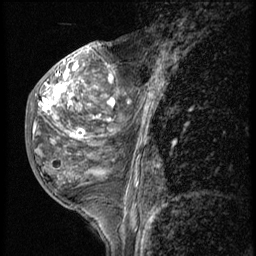
Breast MRI (dynamic contrast-enhanced), one sagittal slice; slice 22 of 56 in the series (ordered by position); 3 images stored at this slice position (order not interpretable as contrast timing); 1.5 T; TE 4.2 ms, TR 9 ms; 2.5 mm slice thickness; 256 × 256 image matrix, field of view 180 × 180 mm. Patient: female, 50 years. From the clinical record (not read from this slice): setting: breast cancer imaged before/during neoadjuvant chemotherapy; receptor status: triple-negative.
Outlined on this slice (semi-automatically segmented with operator editing):
- analysis volume of interest (the breast-tissue region the enhancement analysis was run in; not a lesion): box from (x=25, y=50) to (x=117, y=191) px
- tumour enhancement mask (voxels above the 140 % enhancement threshold inside the analysis volume of interest): (x=42, y=68)–(x=114, y=138)